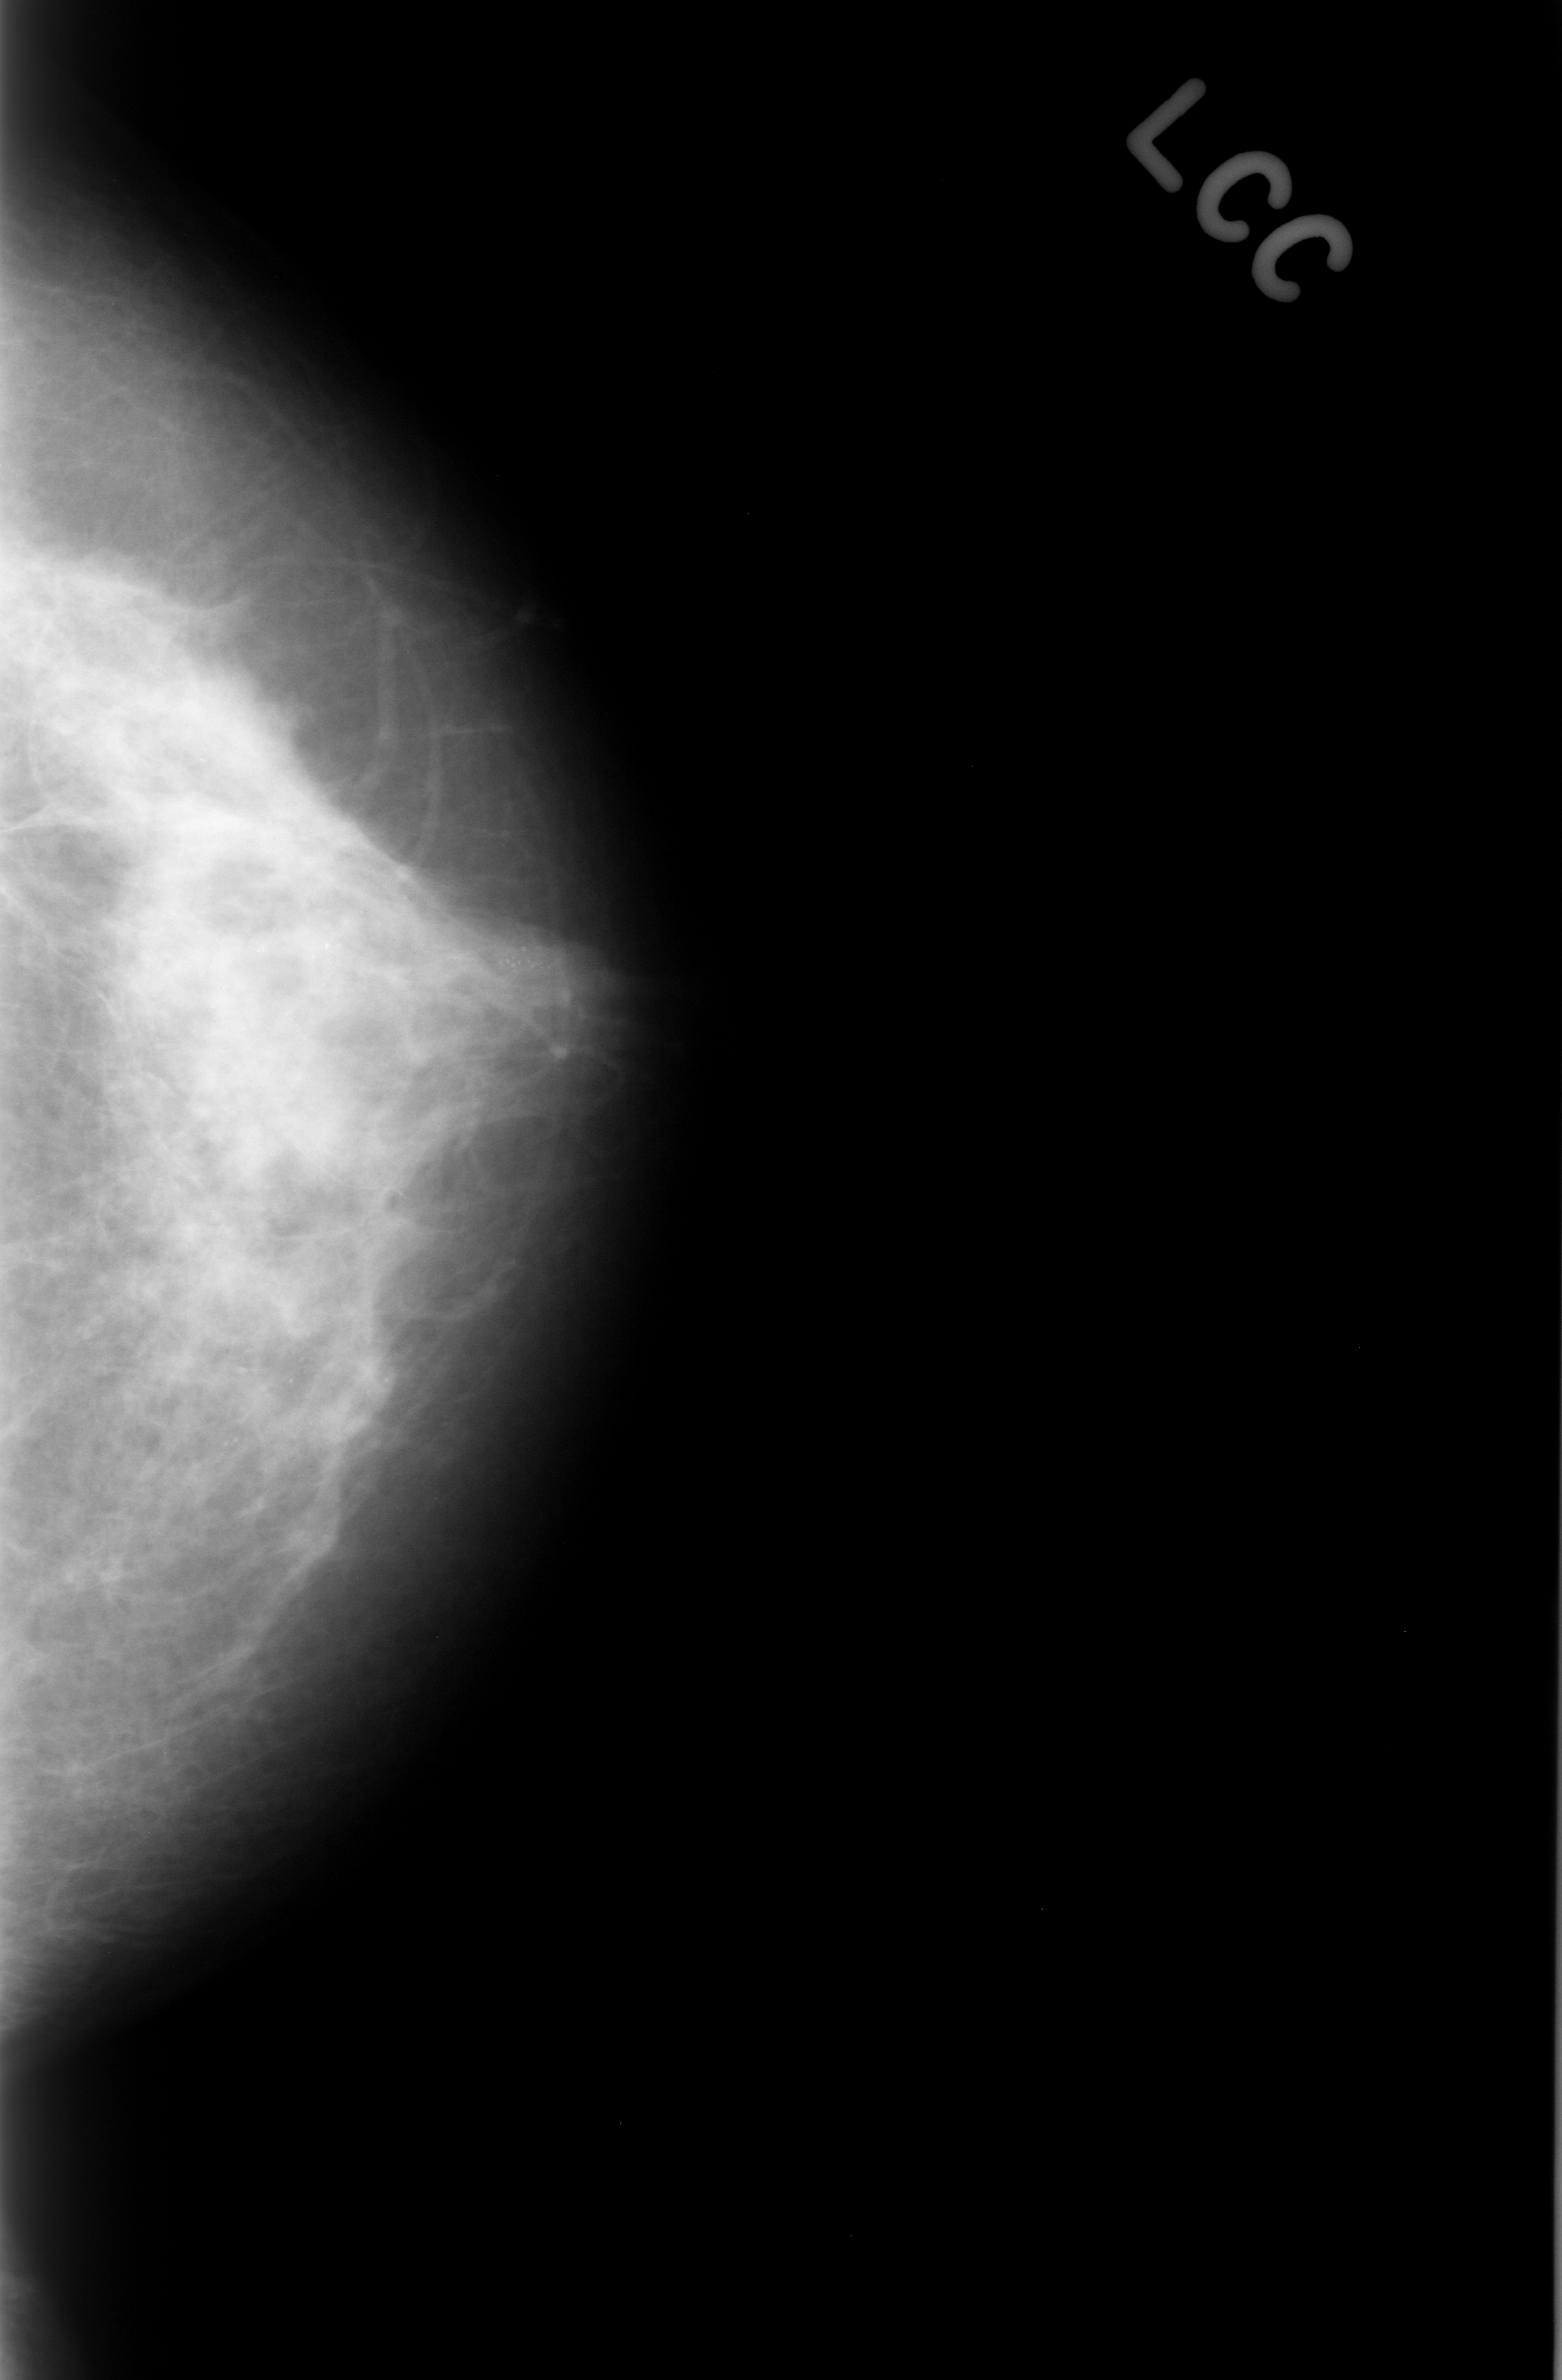
Scanned film-screen mammogram; left breast; craniocaudal (CC) view; breast composition: heterogeneously dense (BI-RADS density category 3 of 4); 1562 × 2380 image matrix.
Expert-marked regions of interest on this film, with their recorded descriptors:
- calcifications, morphology punctate, distribution clustered; BI-RADS assessment category 4; pathology (as recorded): benign: bounding box (x1, y1, x2, y2) in pixels: (404, 890, 582, 1060)